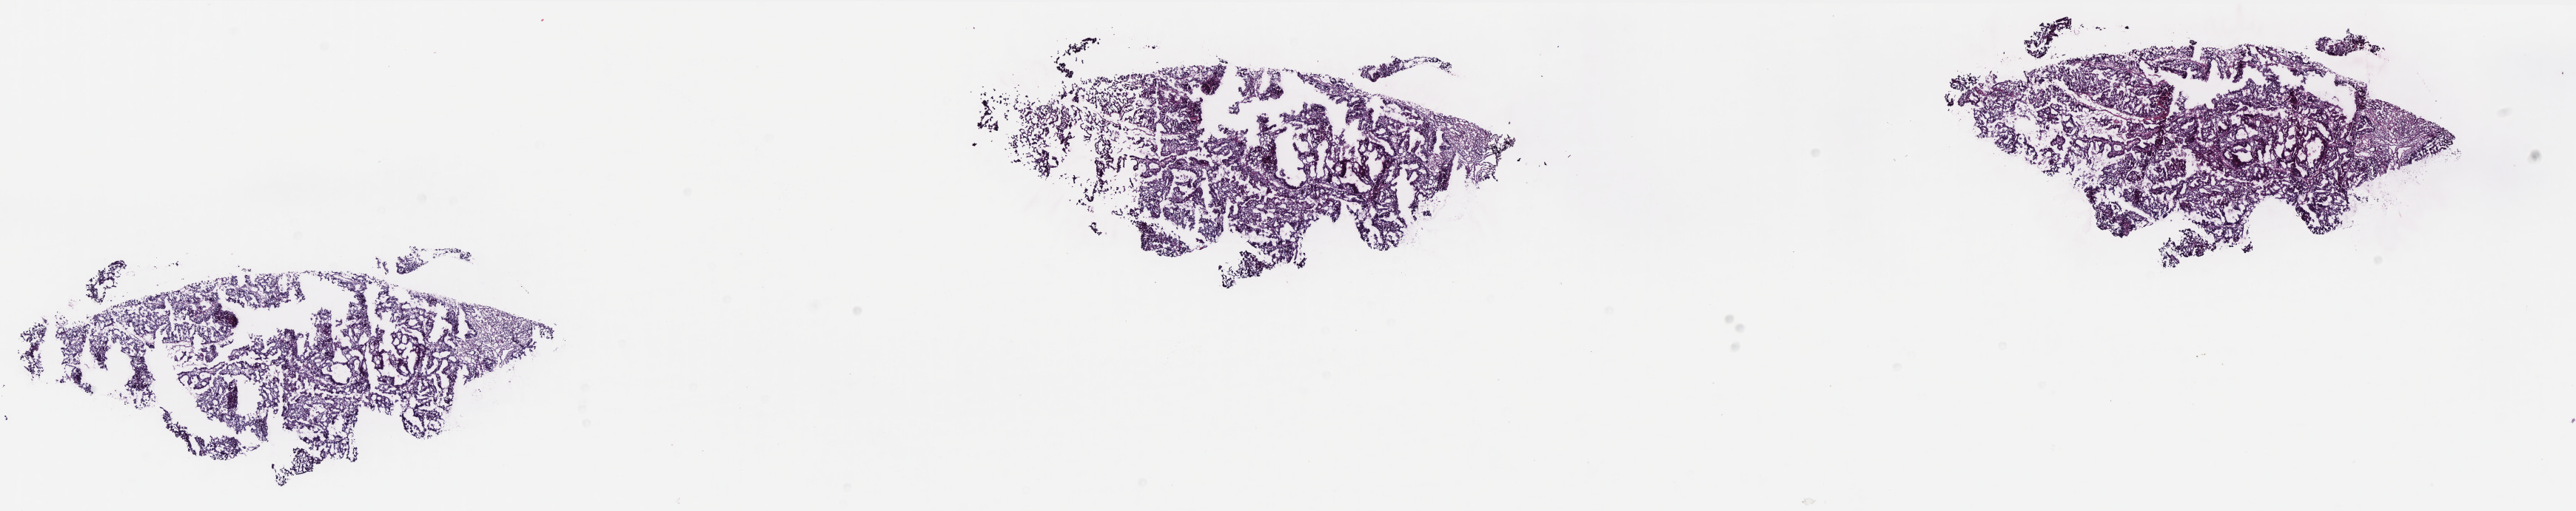
Whole-slide histology image, Hematoxylin and eosin (H&E) stained, shown as a low-resolution overview of the whole scanned area (about 27.9 x 5.5 mm); frozen section from the top of the tissue portion; uterus, primary tumour sample. Female, age 58 years at initial diagnosis. Histologic grade: G1 (well differentiated). Pathologist review of this section (percent, as recorded): tumour cells 100%, tumour nuclei 90%, normal cells 0%, stromal cells 0%, necrosis 0%. Inflammatory infiltration, as recorded: lymphocyte infiltration 1%, monocyte infiltration 0%, neutrophil infiltration 0%.
Diagnosis: Endometrioid adenocarcinoma, NOS. FIGO stage: IA. Lymph nodes positive (case pathology): 0 of 1 examined.